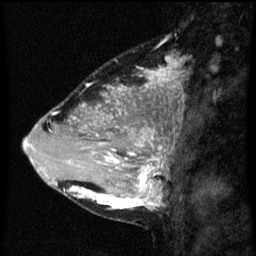
Breast MRI (dynamic contrast-enhanced), one sagittal slice; position 22 of 60 along the scan axis; dynamic contrast-enhanced series, image 2 of 3 at this slice position (ordered by acquisition); 1.5 T; TE 4.2 ms, TR 8 ms; 2.3 mm slice thickness; 256 × 256 image matrix, field of view 180 × 180 mm. Patient: female, 33 years.
Structures marked on this image (semi-automatically segmented with operator editing):
- analysis volume of interest (the breast-tissue region the enhancement analysis was run in; not a lesion): bounding box [x1, y1, x2, y2] px = [71, 118, 169, 209]
- tumour enhancement mask (voxels above the 70 % enhancement threshold inside the analysis volume of interest): [73, 128, 163, 209]